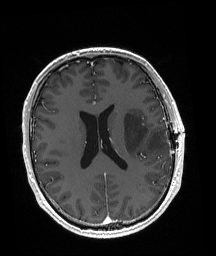
Brain MRI from a brain-tumour surgery series, one axial slice; position 82 of 192 along the scan axis; T1-weighted post-contrast; 1 mm slice thickness; 216 × 256 image matrix, field of view 211 × 250 mm. Case-level facts recorded for this patient, not image findings: histopathology: Astrocytoma; WHO grade: 3; IDH mutation: yes; tumour location: Left Posterior Frontal.
Outlined on this slice (manually delineated by an expert):
- tumour: bounding box (x1, y1, x2, y2) in pixels: (124, 112, 167, 155)